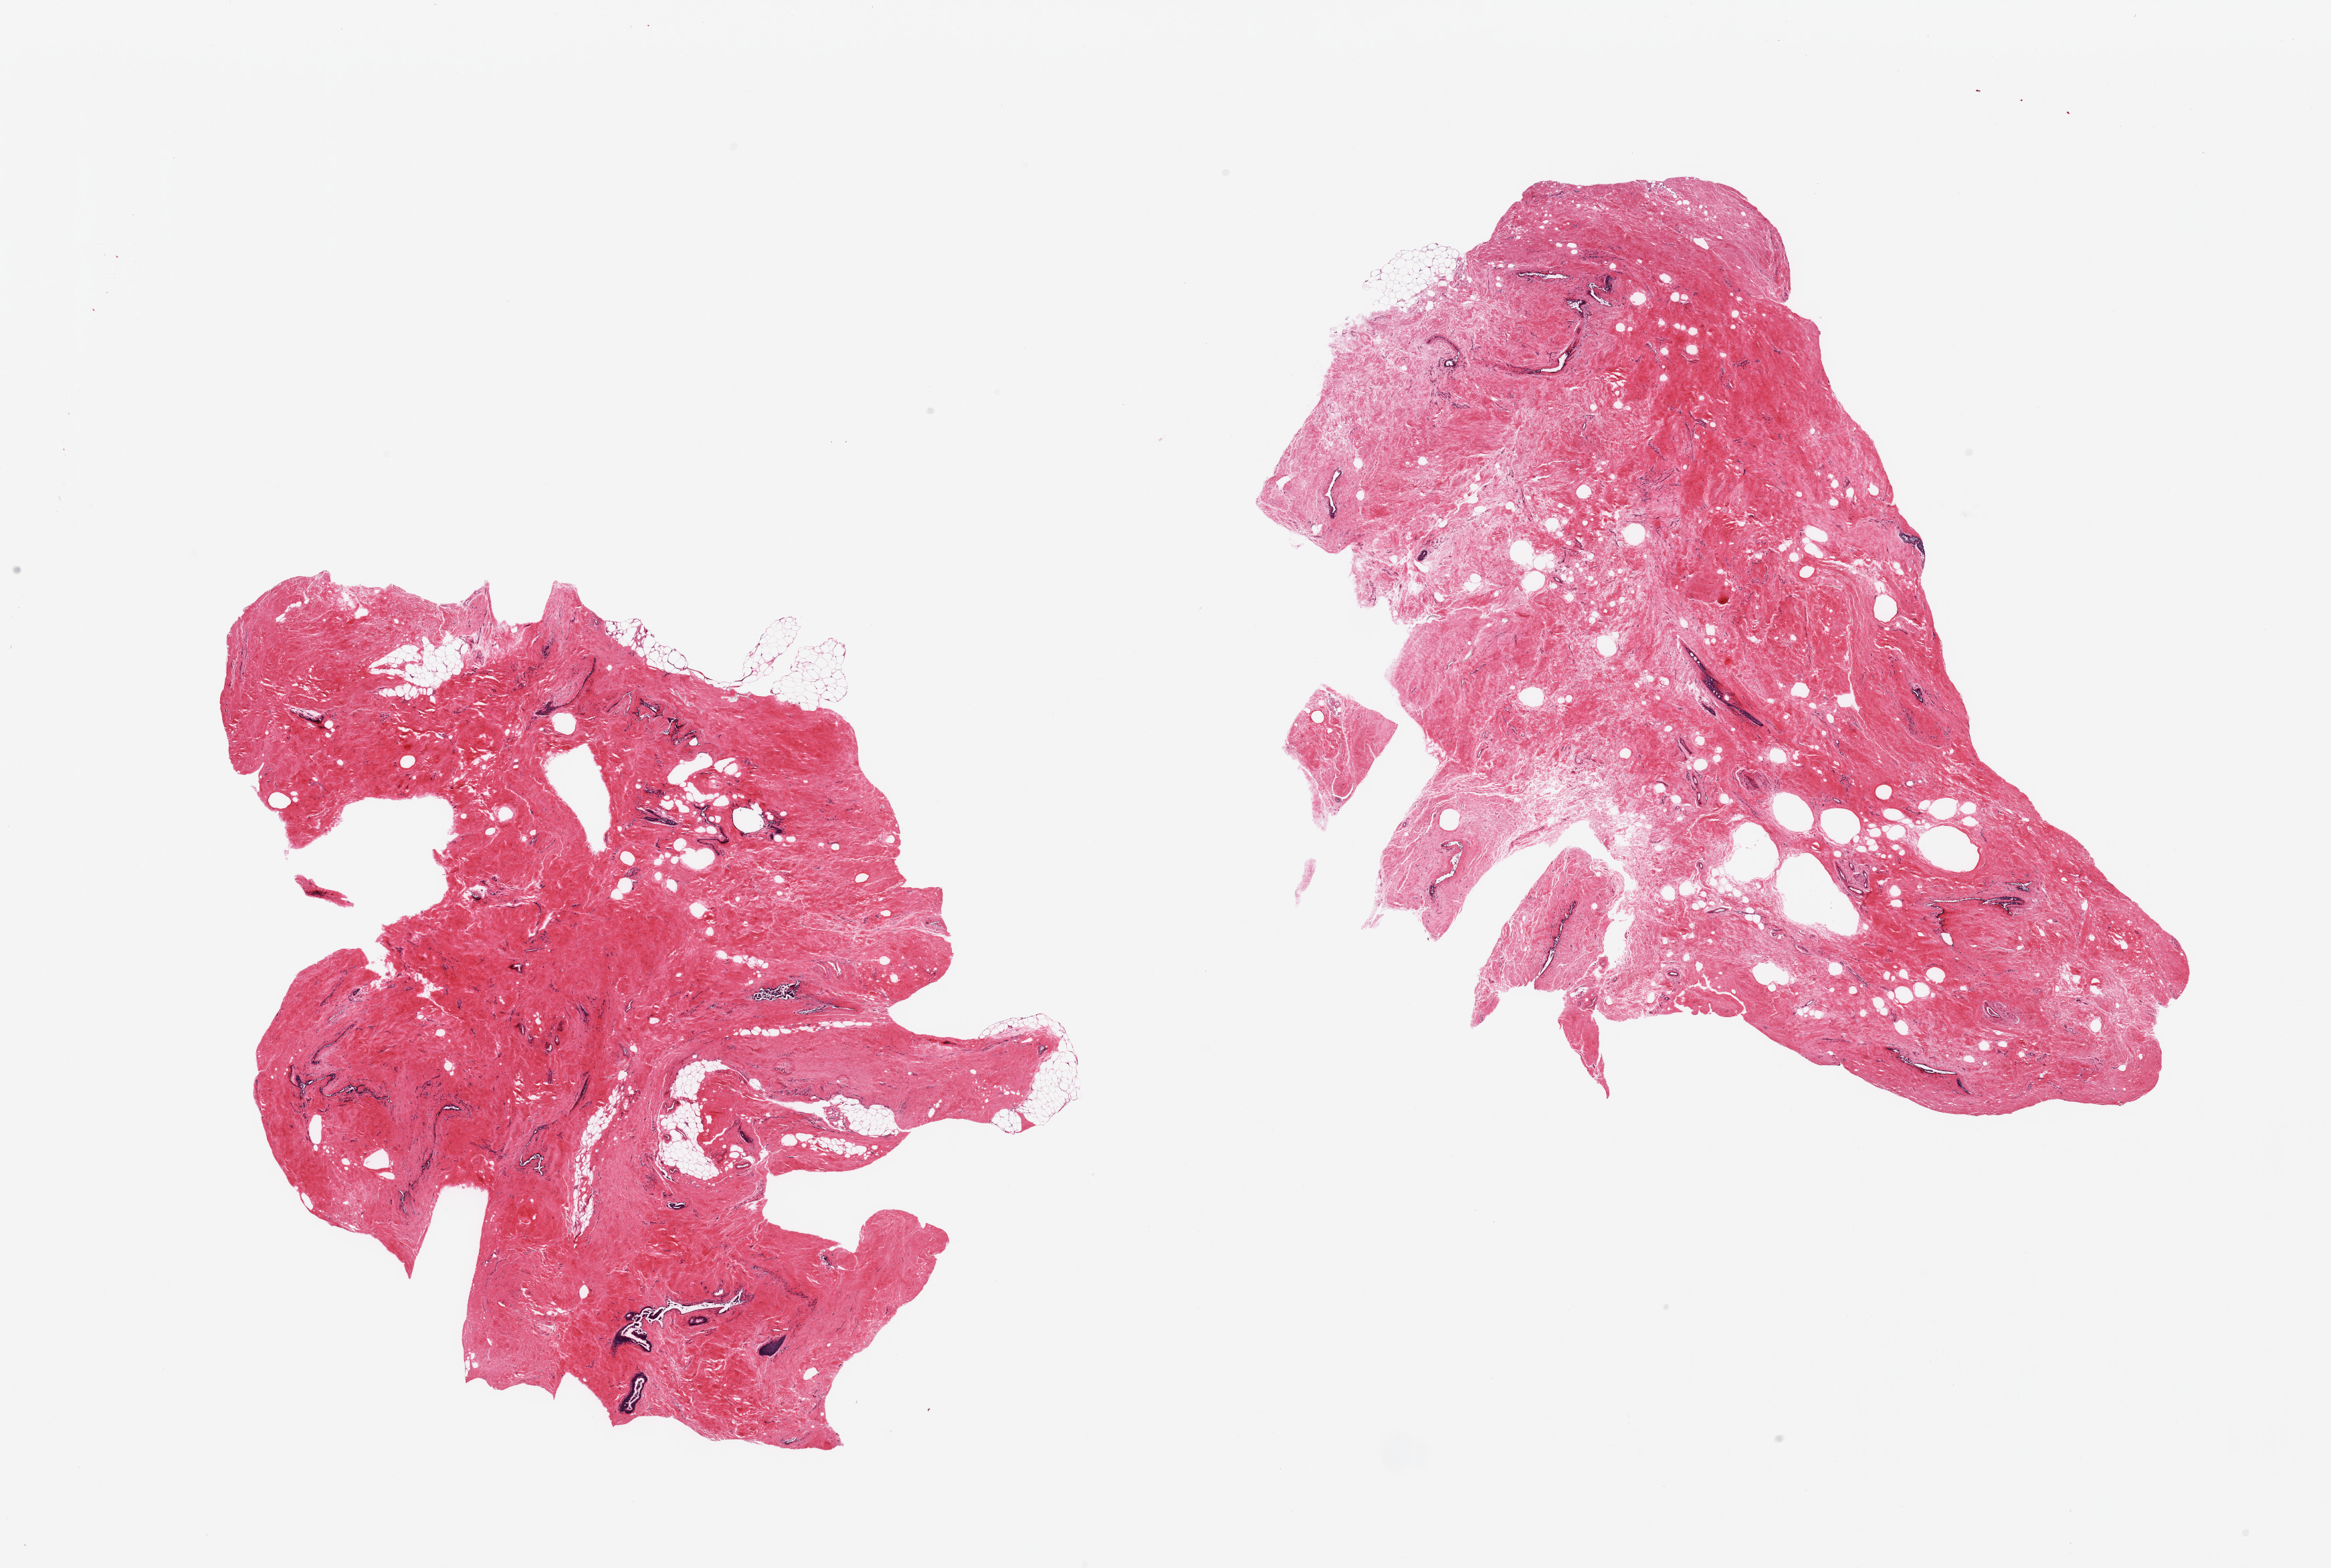
H&E whole-slide image, brightfield — shown as a low-resolution overview of the whole scanned area (about 27.6 x 18.5 mm), PAXgene-fixed paraffin-embedded (PFPE) section, target tissue: breast, tissue donor sample. Donor: male.
• pathologist's review note for this sample: 2 pieces; gynecomastoid features: prominent ducts in fibrous stroma